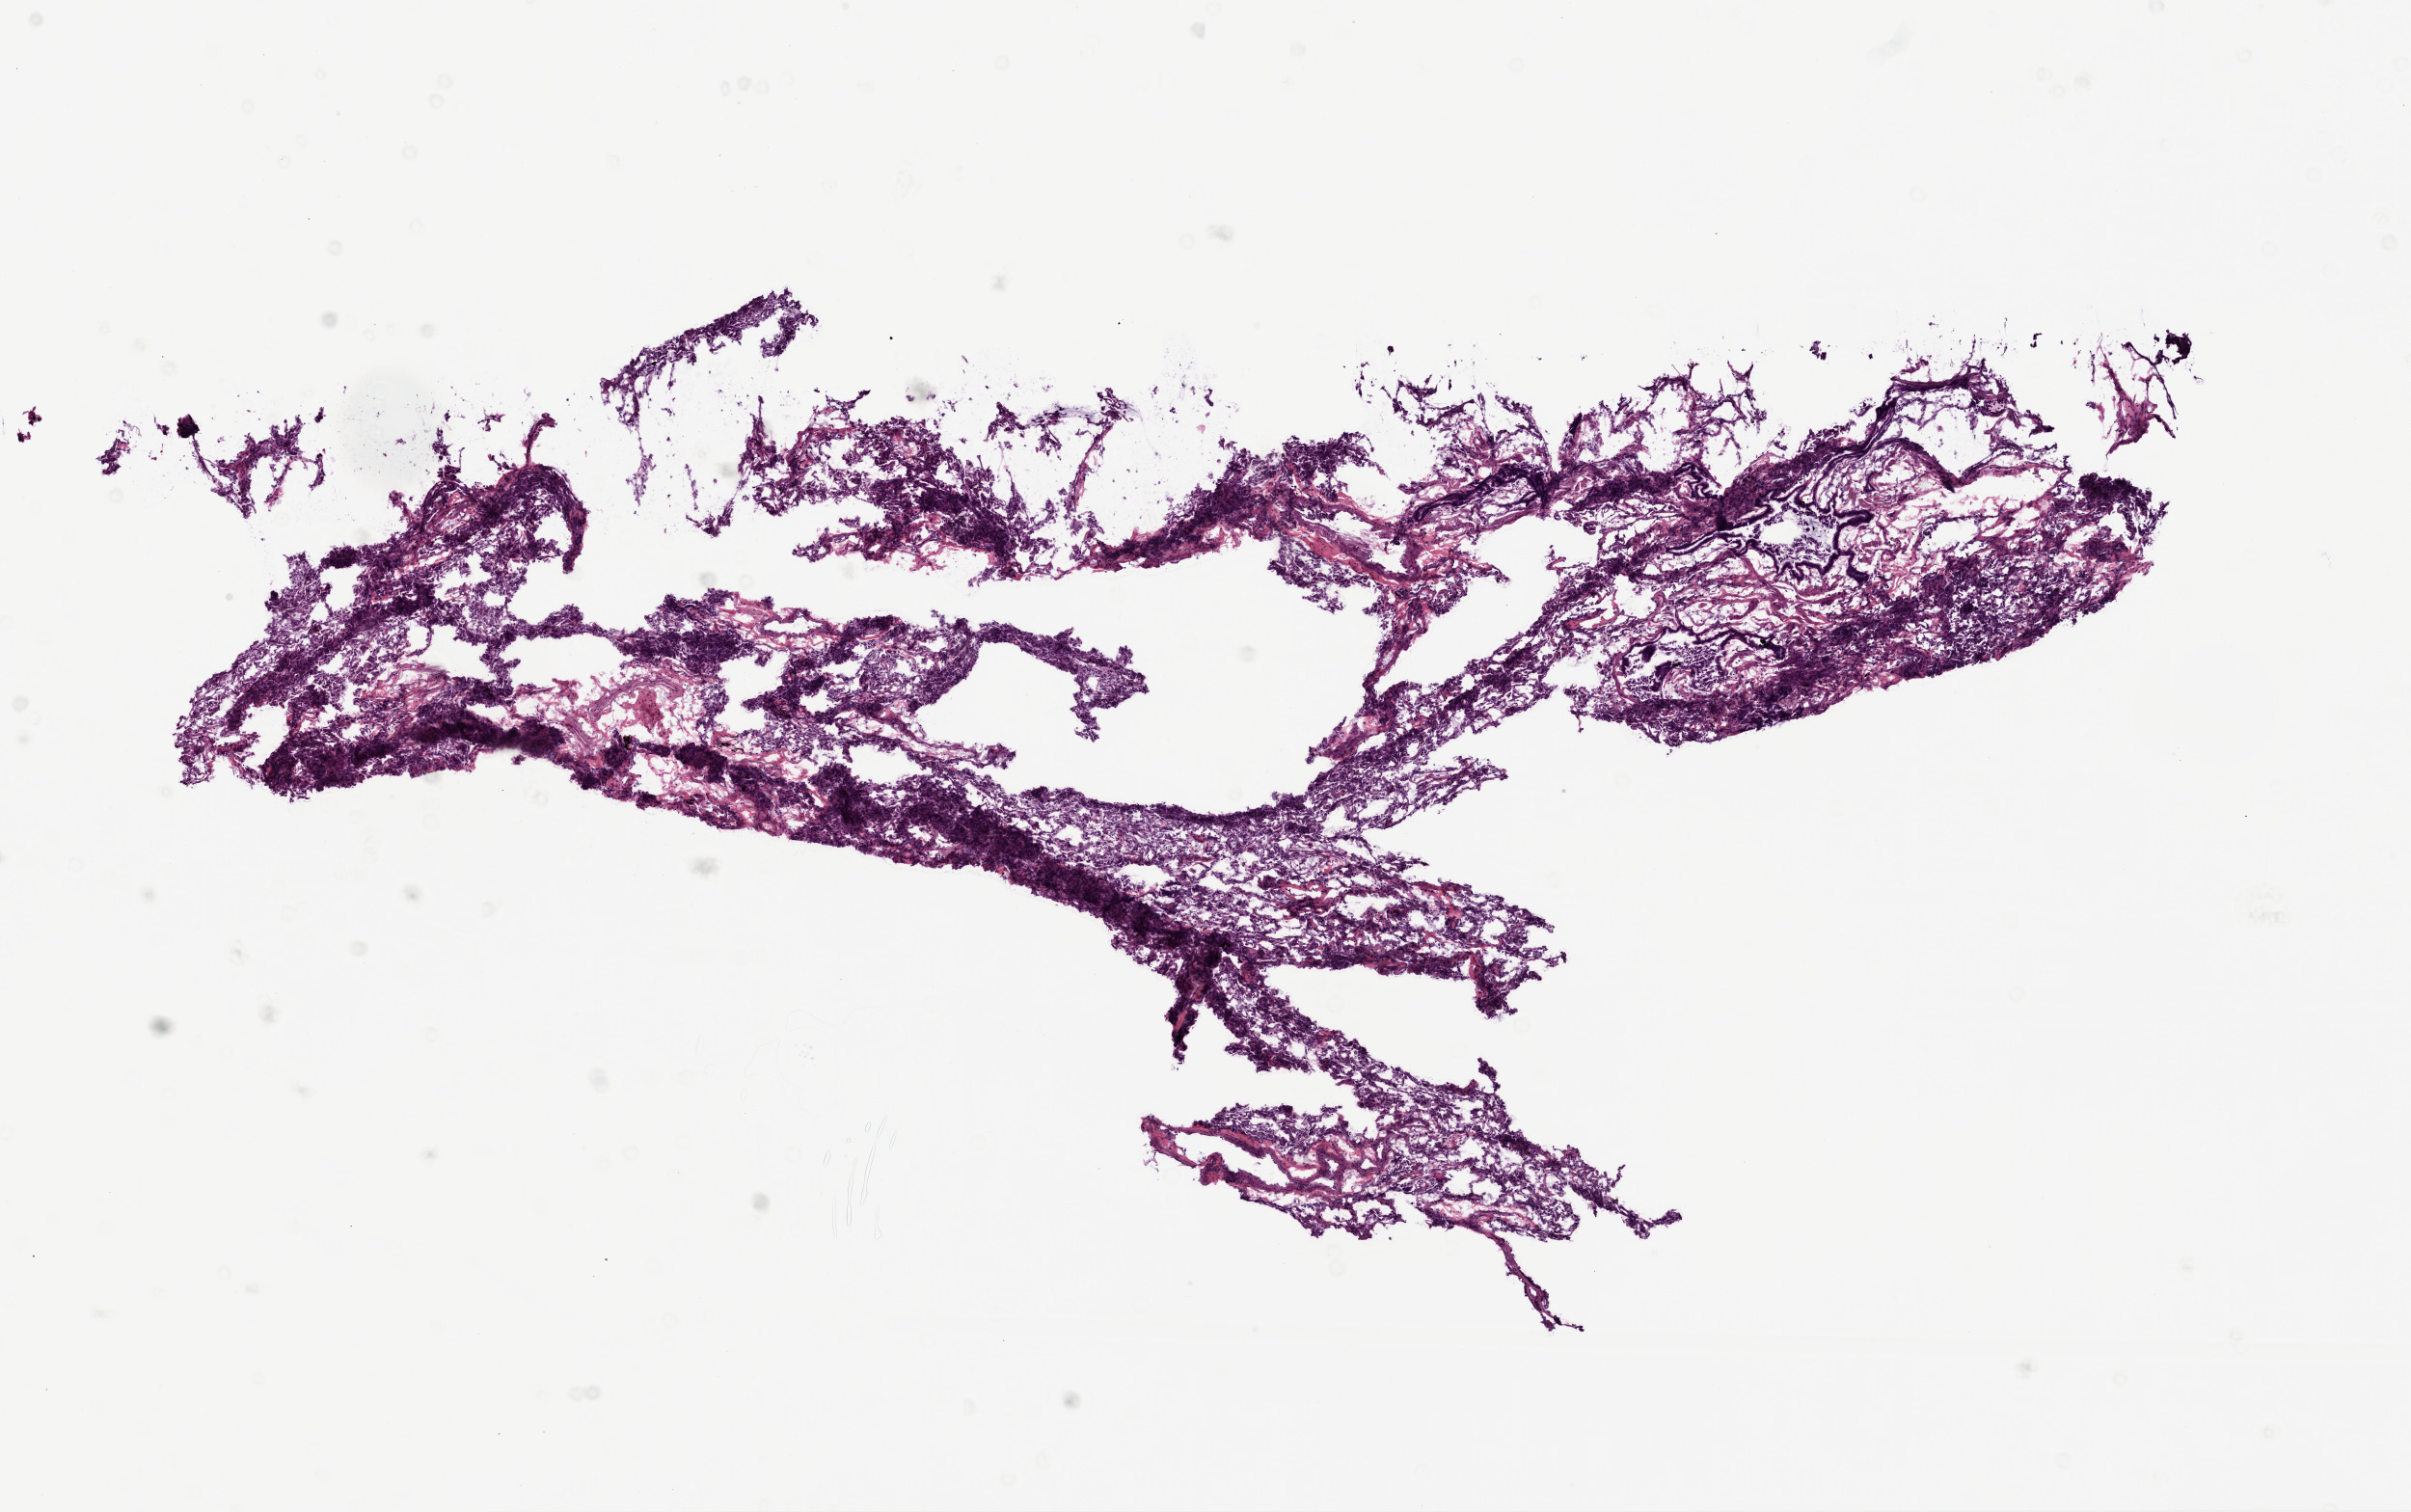
Digitized H&E tissue section (whole slide) — a low-resolution overview of the entire scanned area, about 10.0 x 6.3 mm (acquisition: 20x scan); frozen section from the top of the tissue portion; sample: solid tissue normal (non-tumour tissue), lung. Male, age 62 years at initial diagnosis.
This section: solid tissue normal sample (biorepository sample class). Patient diagnosis: Squamous cell carcinoma, NOS (lower lobe, lung).